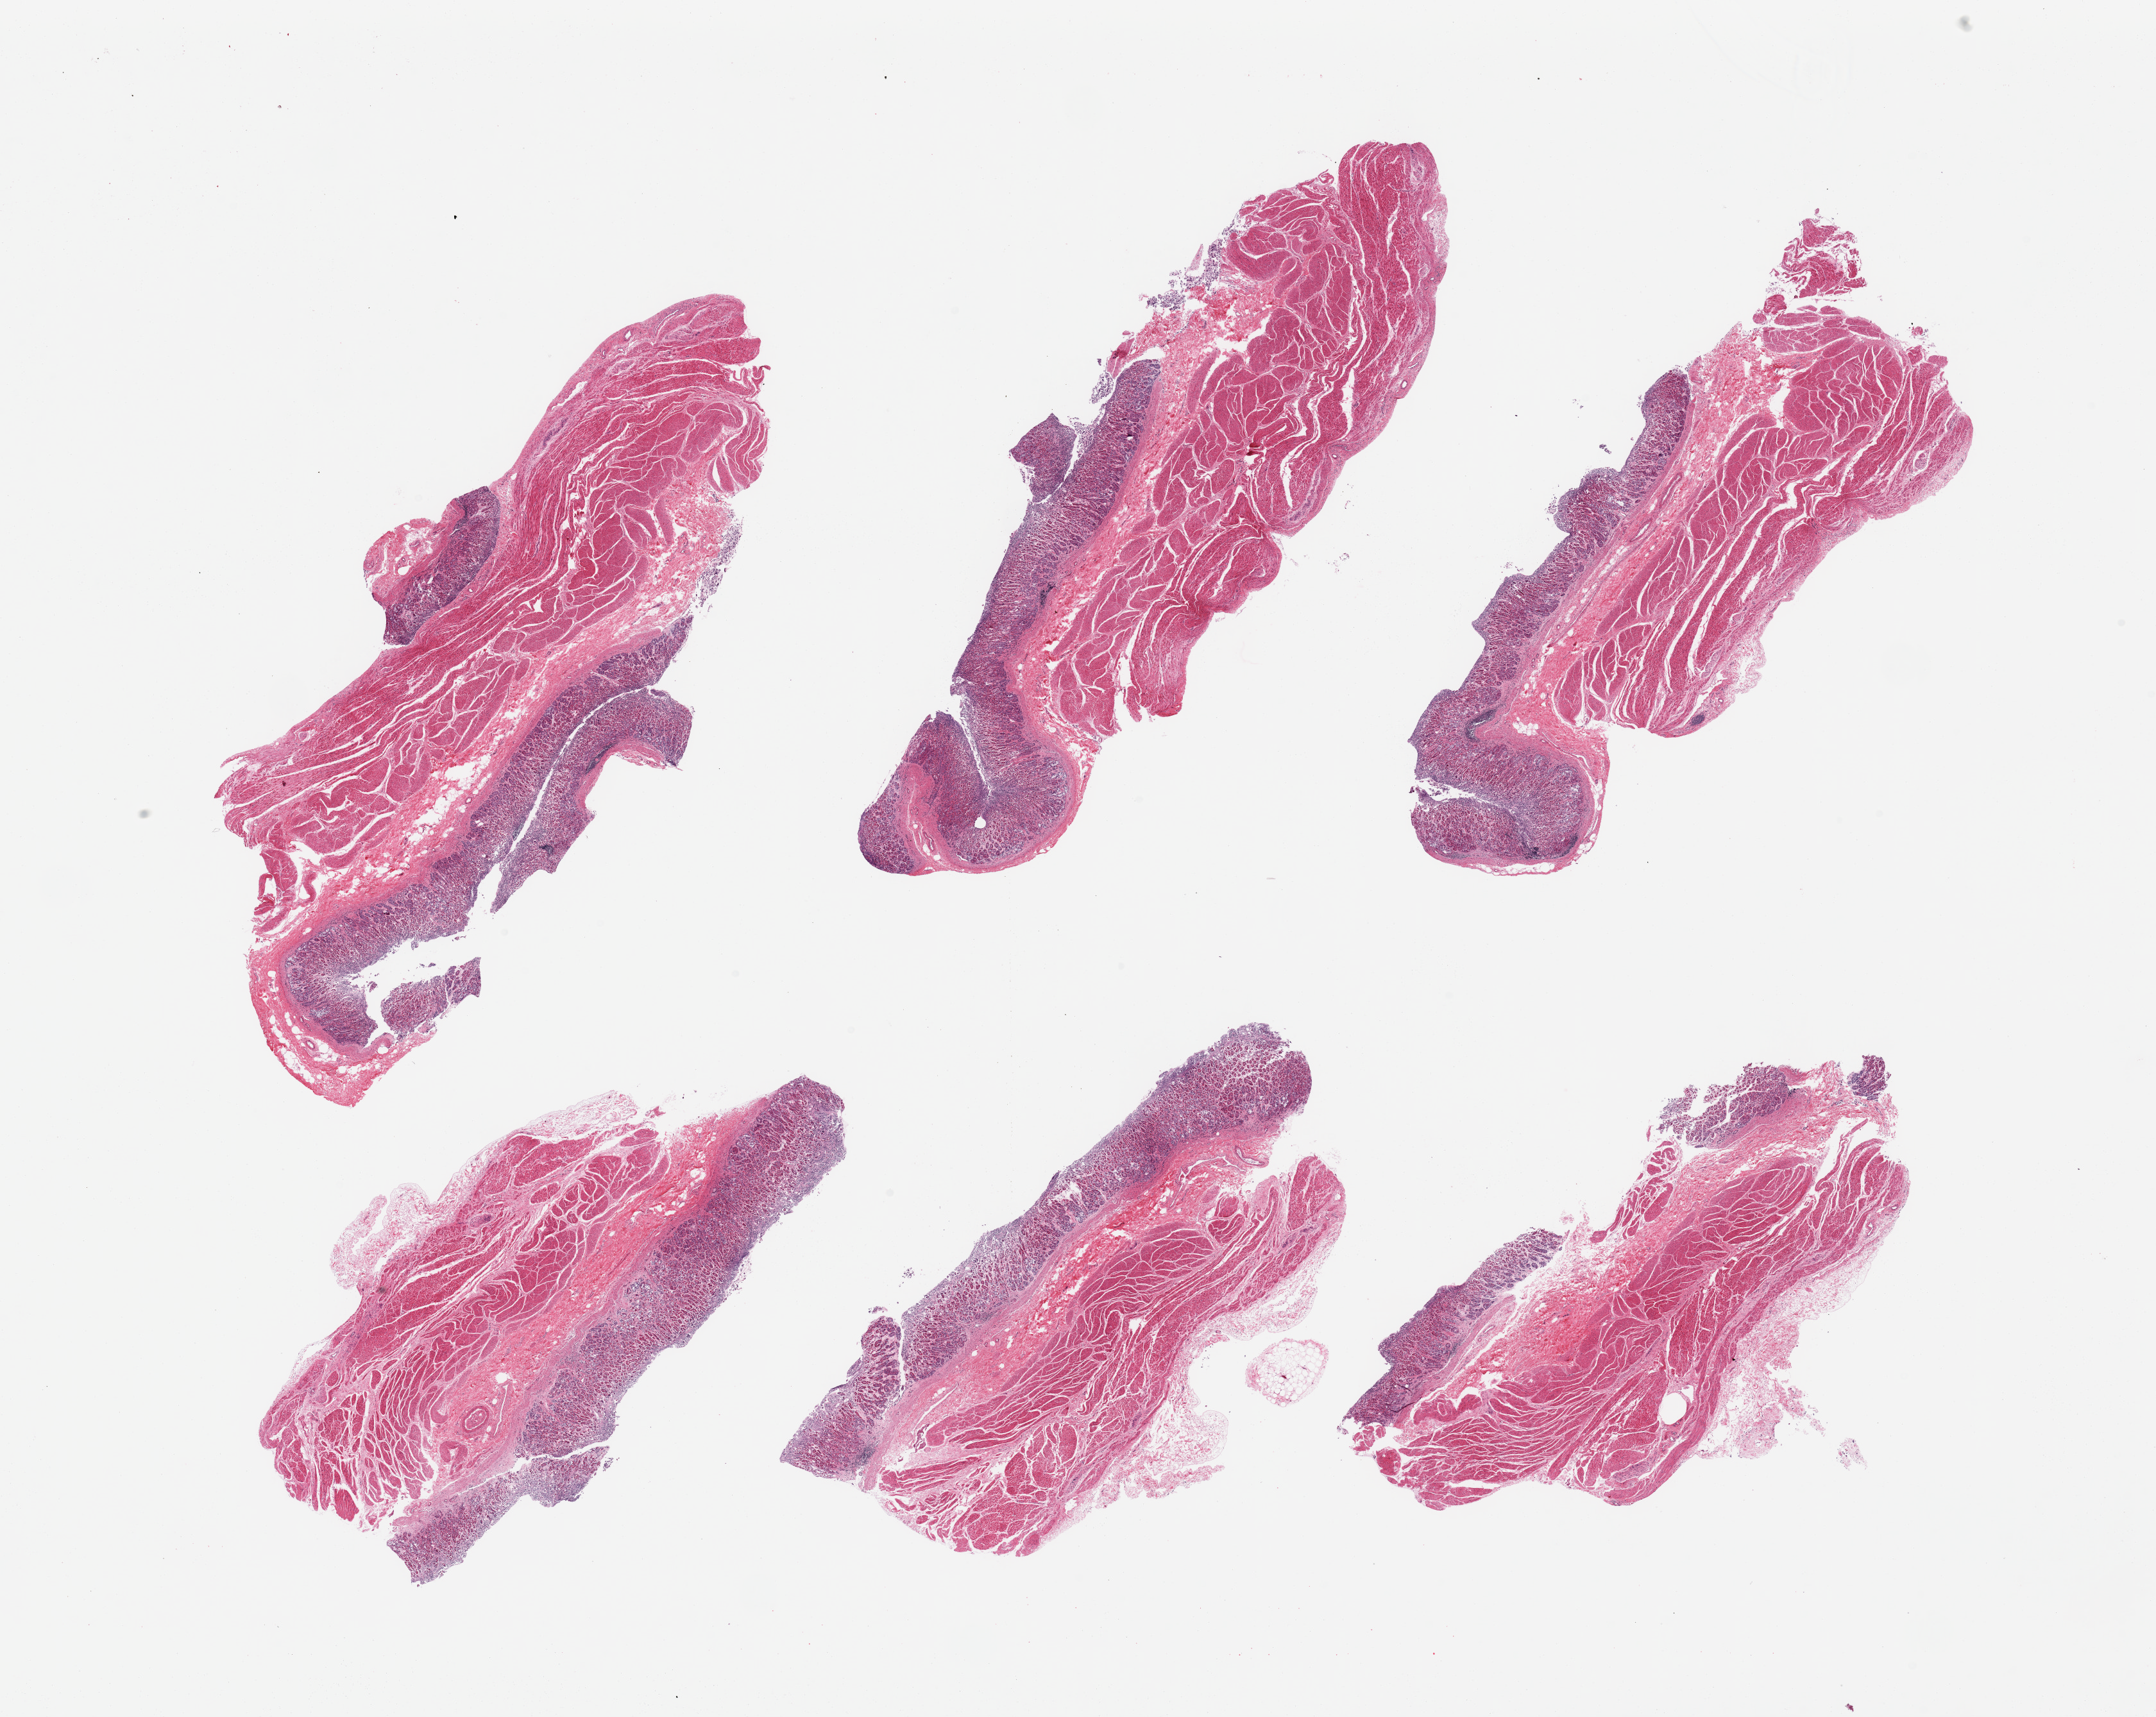
Whole-slide image, haematoxylin and eosin stain — whole scanned area (about 26.6 x 21.2 mm) shown as a low-resolution overview, PAXgene-fixed, paraffin-embedded tissue, sampled site (target tissue): stomach, tissue donor sample. Male donor.
• pathologist's review note for this sample: 6 pieces; full thickness sections, mild chronic inflammation